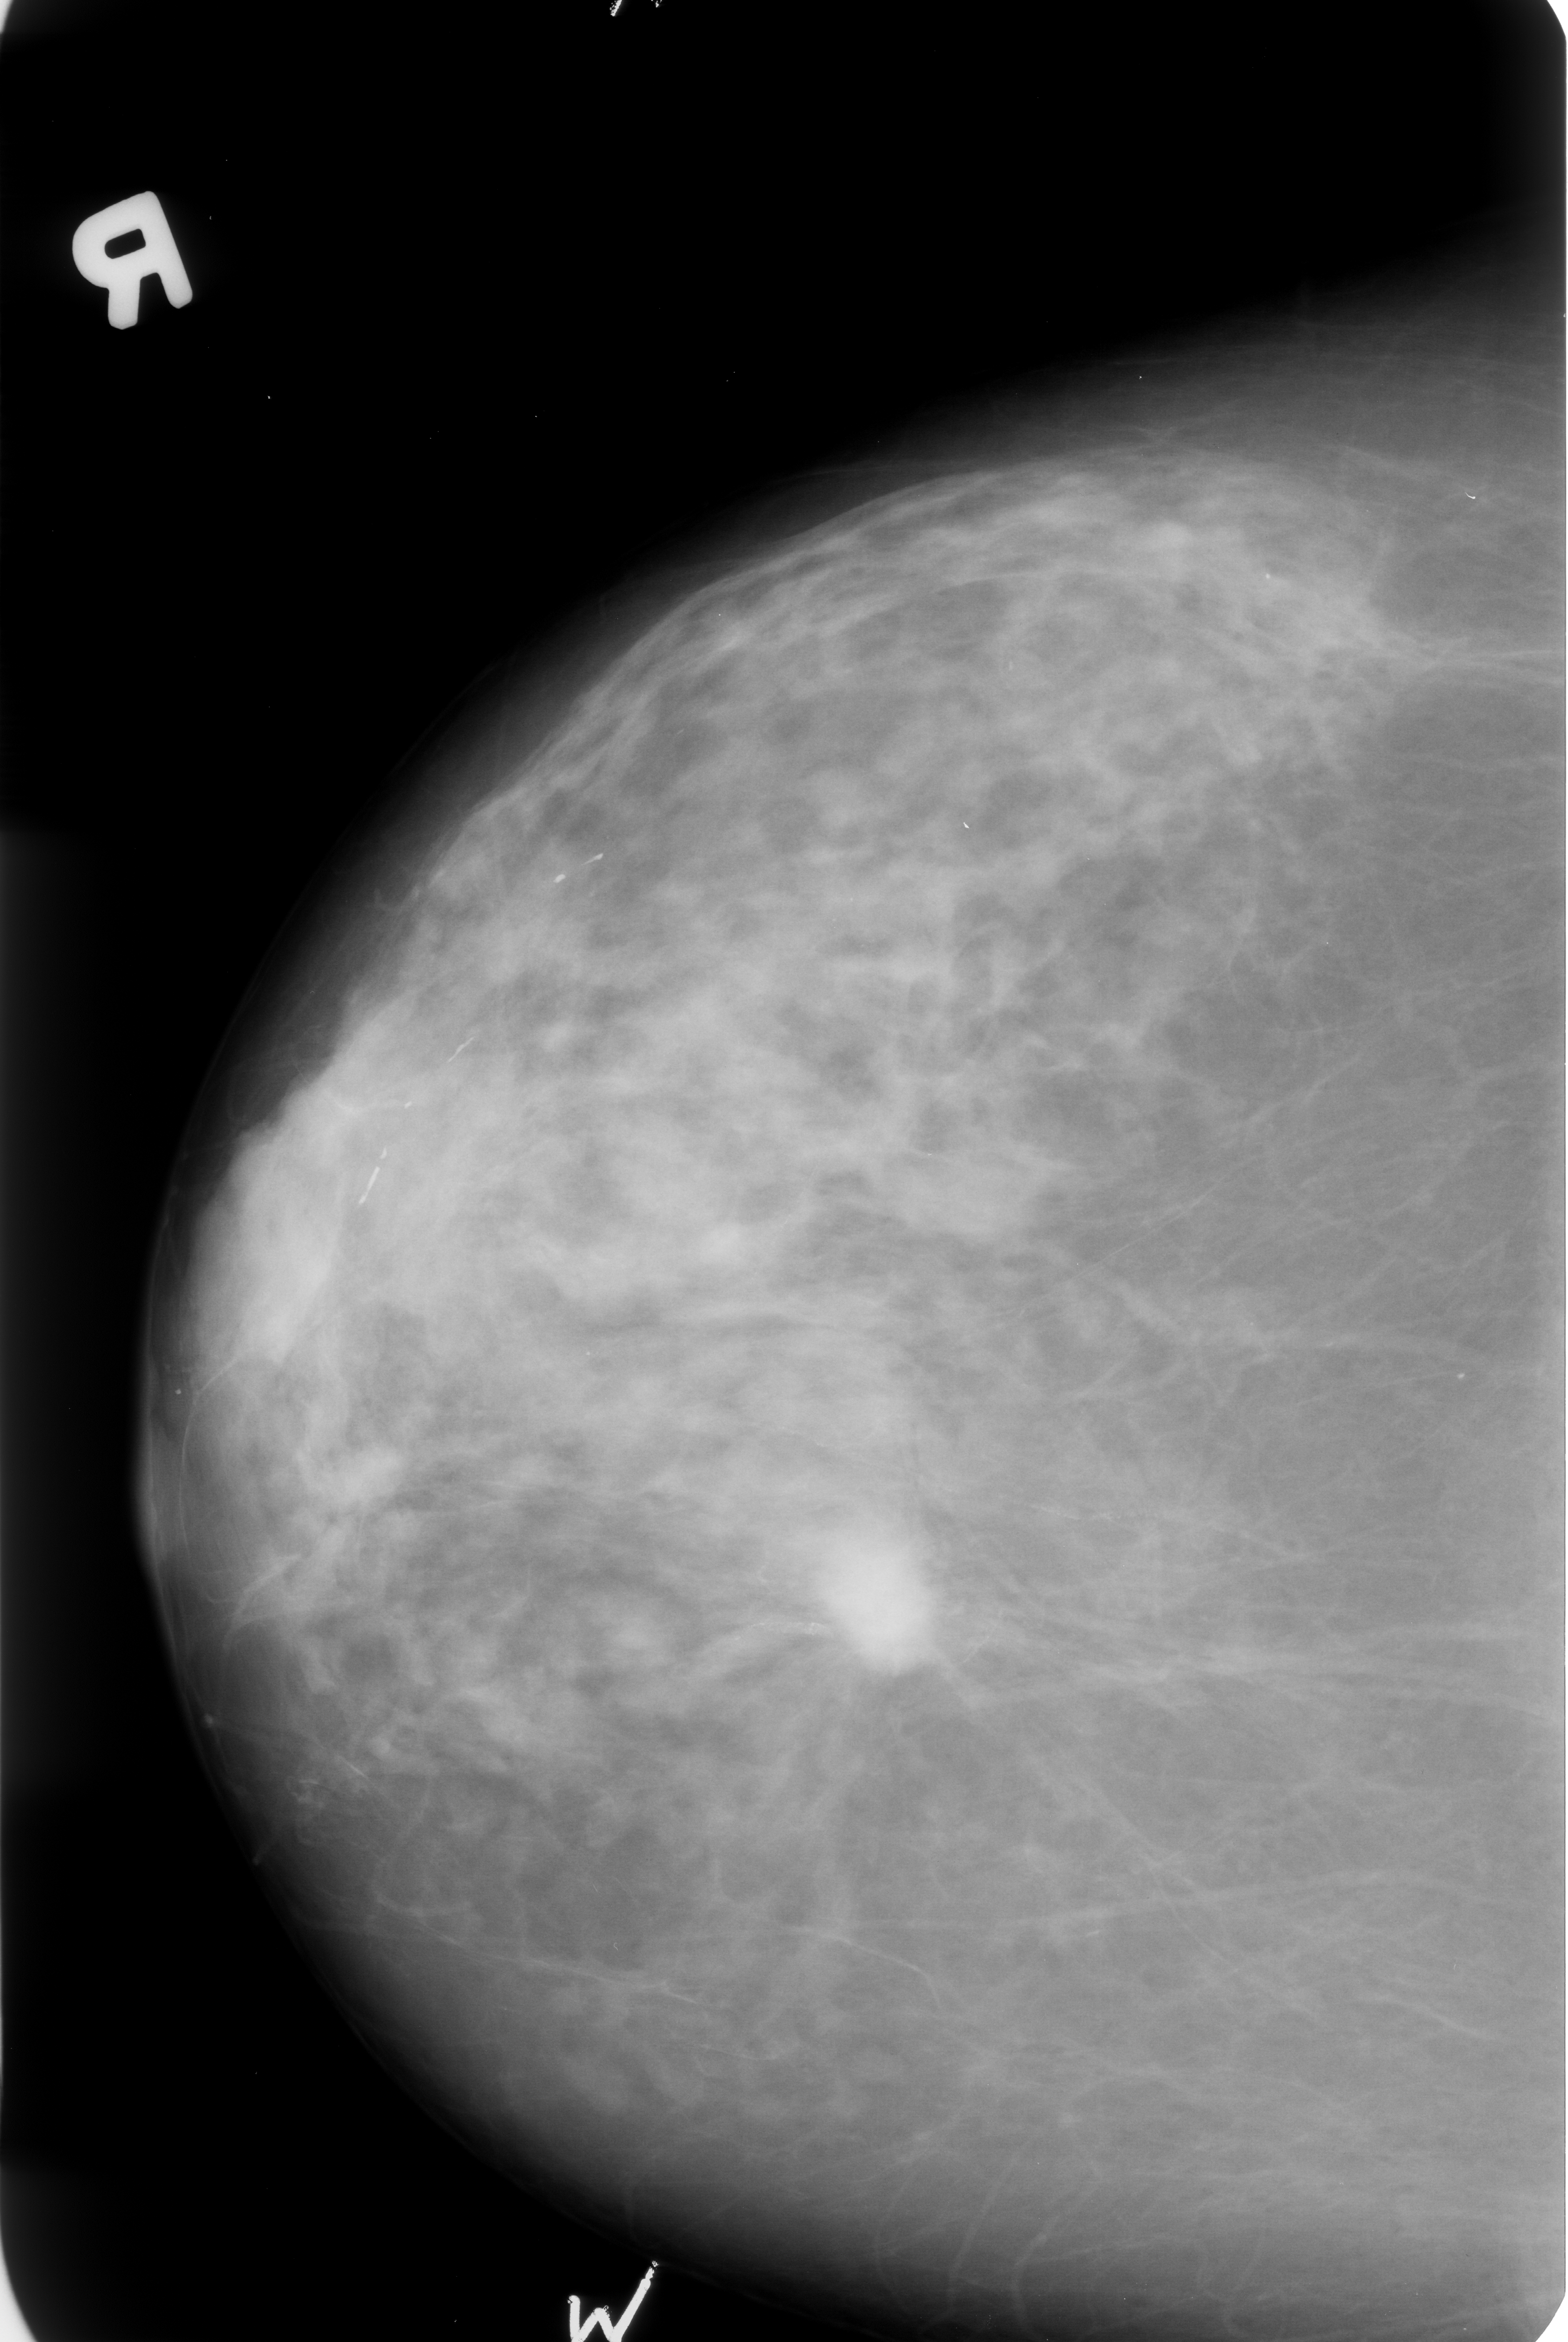
Mammogram (digitized film). Right breast. Craniocaudal (CC) view. Breast composition: heterogeneously dense (BI-RADS density category 3 of 4). 1568 × 2342 image matrix.
Expert-marked regions of interest on this film, with their recorded descriptors:
- mass, shape irregular / architectural distortion, margins spiculated; BI-RADS assessment category 5; subtlety rating 5 on a 1 (subtle) to 5 (obvious) scale; pathology (as recorded): malignant: bounding box (x1, y1, x2, y2) in pixels: (808, 1517, 947, 1677)